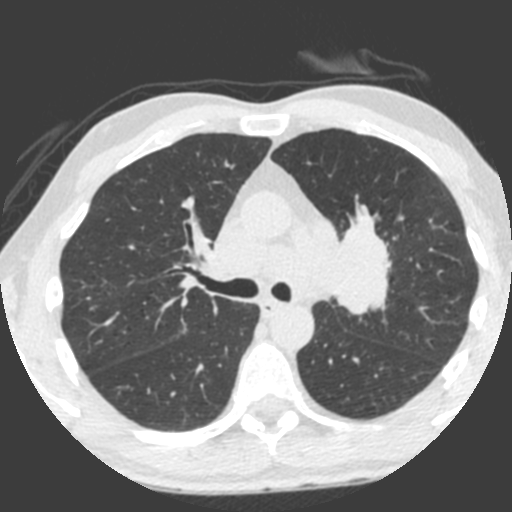
Axial slice from a low-dose chest CT screening exam, third screening round (two years after baseline), lung window (W 1500 / L -600 HU), 2 mm slice thickness, standard (soft-tissue) reconstruction kernel (B), slice 141 of 212 in the series, 512 × 512 image matrix, field of view 315 × 315 mm. Male participant, aged 55 years at enrolment.
Expert-annotated lung lesion, bounding box [x1, y1, x2, y2] px = [309, 223, 395, 324]. Screening reader's record for this exam (one nodule recorded; not confirmed to be the boxed lesion): non-calcified nodule or mass ≥4 mm, left upper lobe, 49 × 29 mm, spiculated (stellate) margins, soft tissue attenuation, pre-existing on the prior screen: yes; interval growth: yes. Official screen result: positive, other. Later outcome: lung cancer diagnosed 0 days after this screen — small cell carcinoma, NOS, left upper lobe, undifferentiated (G4), stage IV (AJCC 6th edition), 60 mm at pathology.